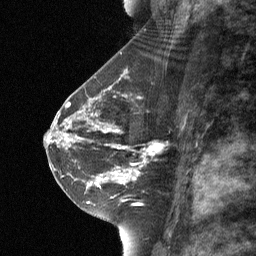
Breast MRI (dynamic contrast-enhanced), one sagittal slice; slice 34 of 64 in the series (ordered by position); dynamic contrast-enhanced study with each time point stored as its own series, time point 2 of 3 at this slice position (early post-contrast, ordered by acquisition time); 1.5 T; TE 4.8 ms, TR 27 ms; 2 mm slice thickness; 256 × 256 image matrix. Patient: female, 42 years. From the clinical record (not read from this slice): setting: breast cancer imaged before/during neoadjuvant chemotherapy; receptor status: triple-negative.
Outlined on this slice (semi-automatic segmentation, software-assisted and operator-edited):
- analysis volume of interest (the breast-tissue region the enhancement analysis was run in; not a lesion): bounding box [x1, y1, x2, y2] px = [111, 124, 156, 178]
- tumour enhancement mask (voxels above the 90 % enhancement threshold inside the analysis volume of interest): [115, 170, 137, 176]